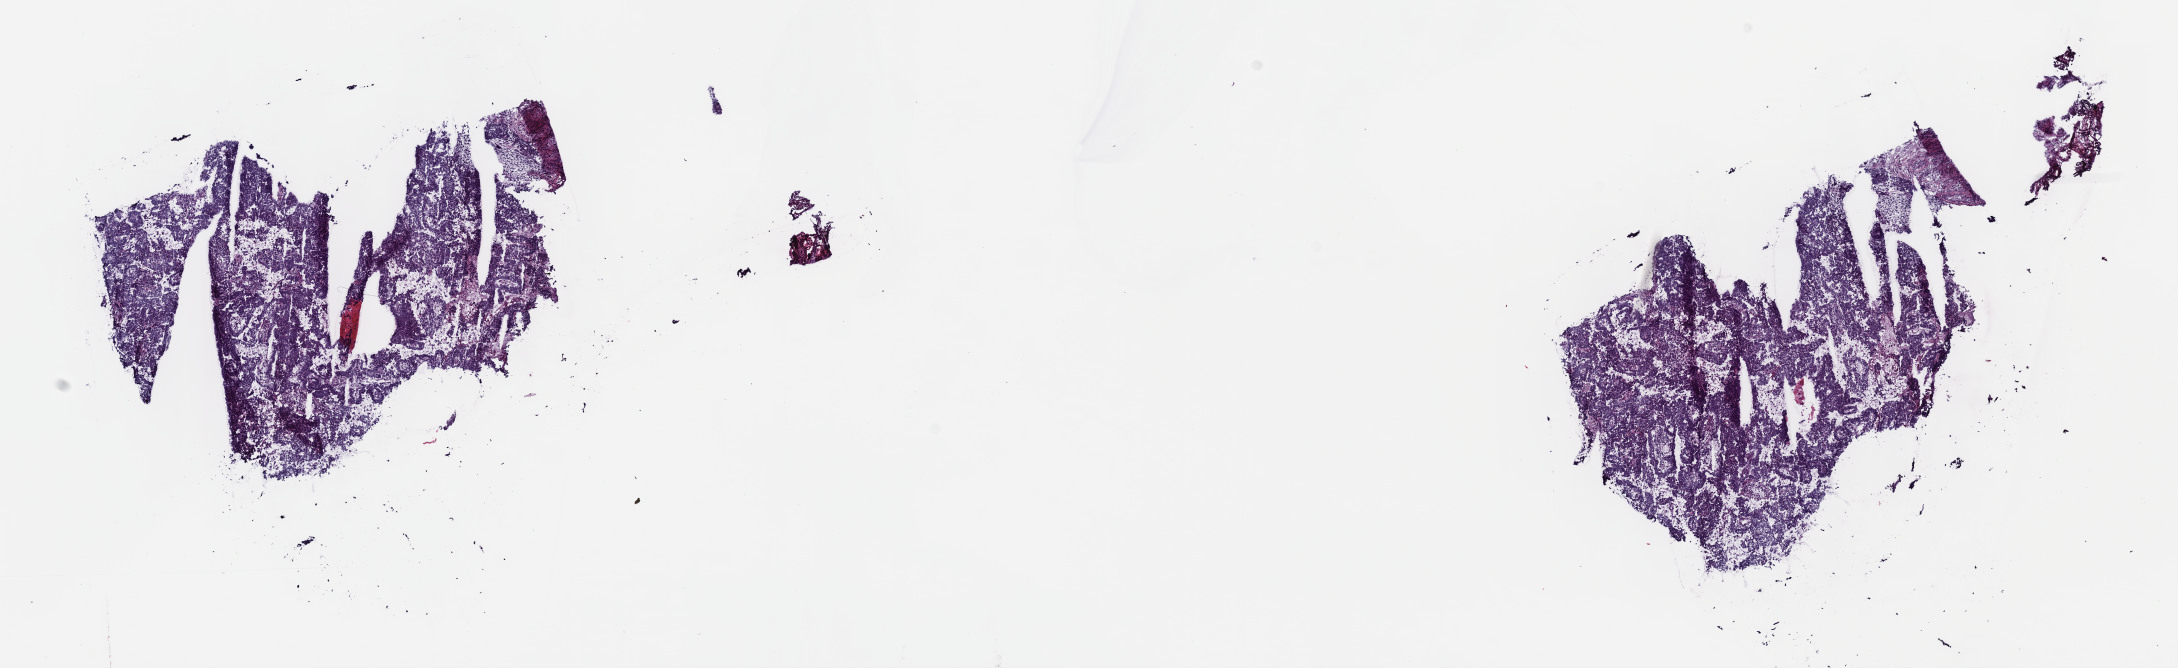
Digitized Hematoxylin and eosin (H&E) stained tissue section (whole slide), a low-resolution overview of the entire scanned area, about 17.6 x 5.4 mm. Frozen section from the top of the tissue portion. Sample: primary tumour, testis. Male, age 26 years at initial diagnosis. Composition of this section per pathologist review: tumour cells 99%, tumour nuclei 80%, normal cells 0%, stromal cells 0%, necrosis 1%. Infiltration values recorded for this section: lymphocyte infiltration 2%, monocyte infiltration 0%, neutrophil infiltration 0%.
Diagnosis: Embryonal carcinoma, NOS. AJCC pathologic stage: IIIB.